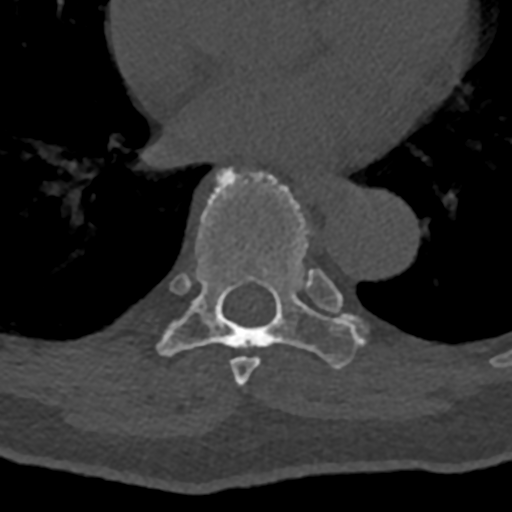
CT including the spine, one axial slice. Slice 720 of 797 in the series (ordered by position). 120 kVp. Bone window (W 1800 / L 400 HU). 0.5 mm slice thickness. 512 × 512 image matrix, field of view 160 × 160 mm. Male patient, age 74 years. Case-level facts recorded for this patient, not image findings: primary cancer: renal.
Annotated regions visible in this slice (semi-automatic segmentation, software-assisted and operator-edited):
- T7 vertebra: bounding box <230,269,340,386> (left, top, right, bottom; pixels)
- T8 vertebra: <157,165,365,369>